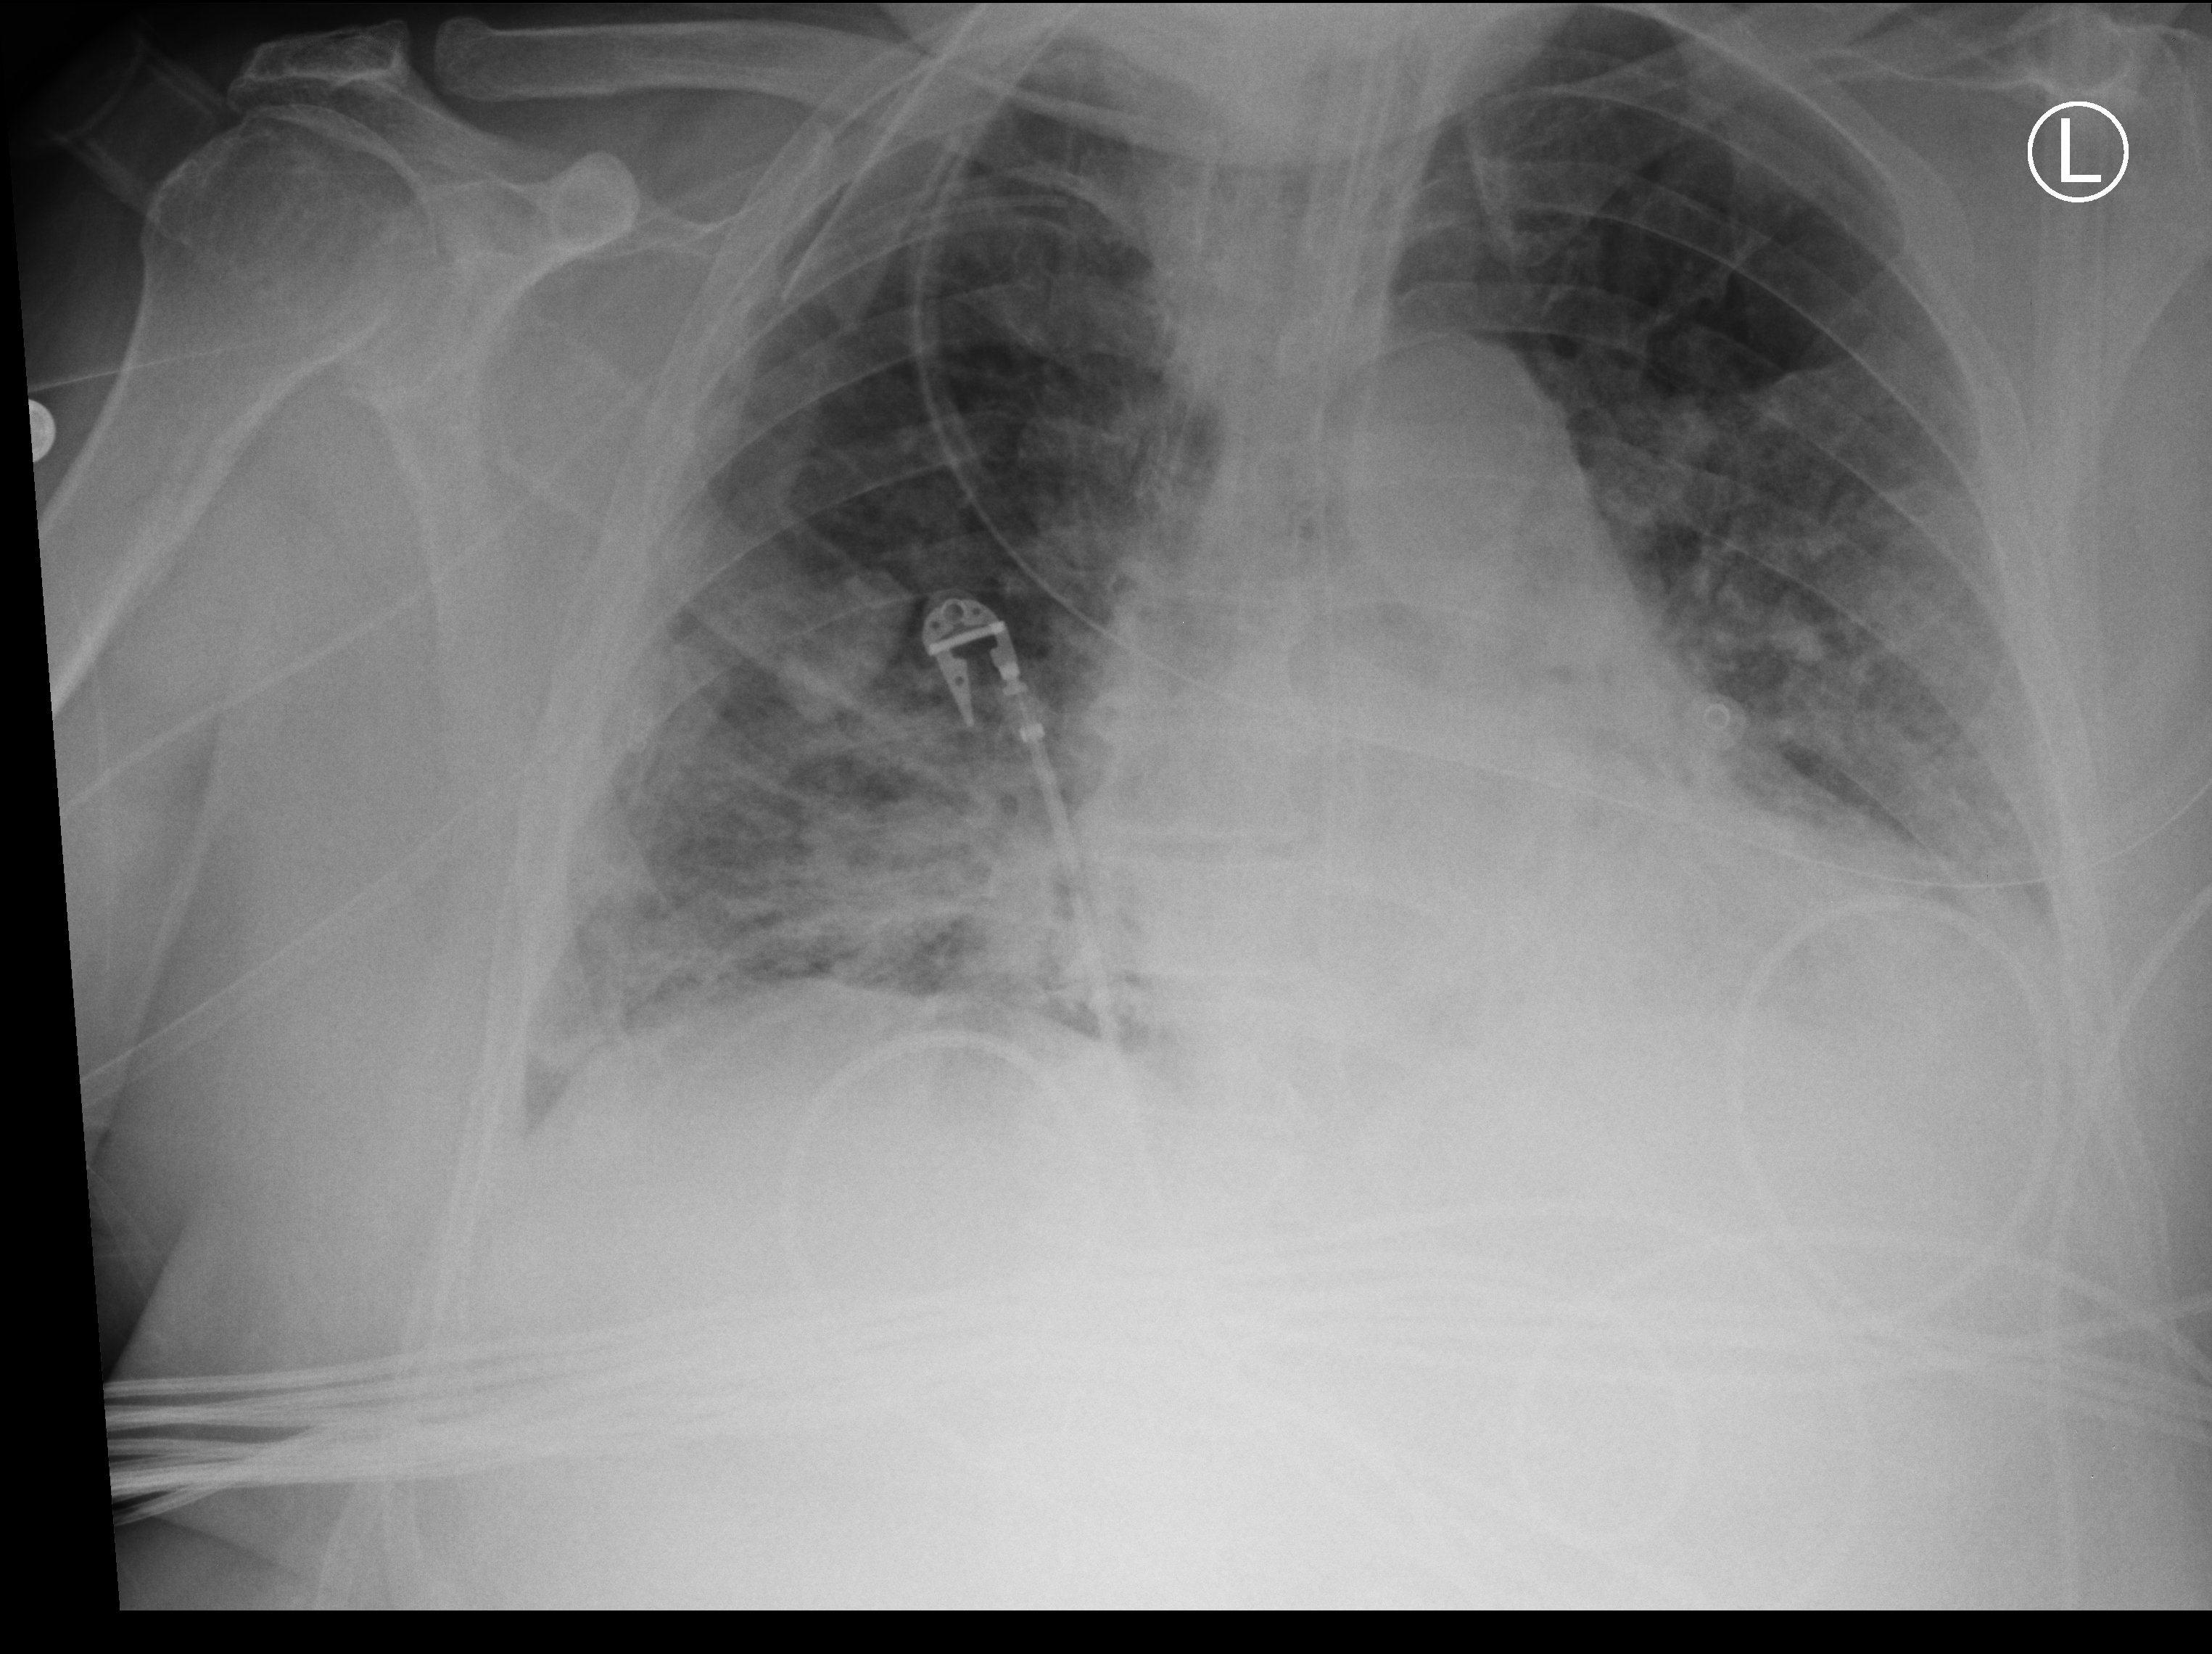
Bedside chest radiograph (computed radiography), anteroposterior (AP) projection. Patient hospitalised with COVID-19; male, aged 60–74 years.
From the hospital-stay record, not from the radiograph (when in the stay this image was taken is not recorded): smoking status (admission record): never; mechanically ventilated during this hospital stay: yes; length of hospital stay: 26 days.